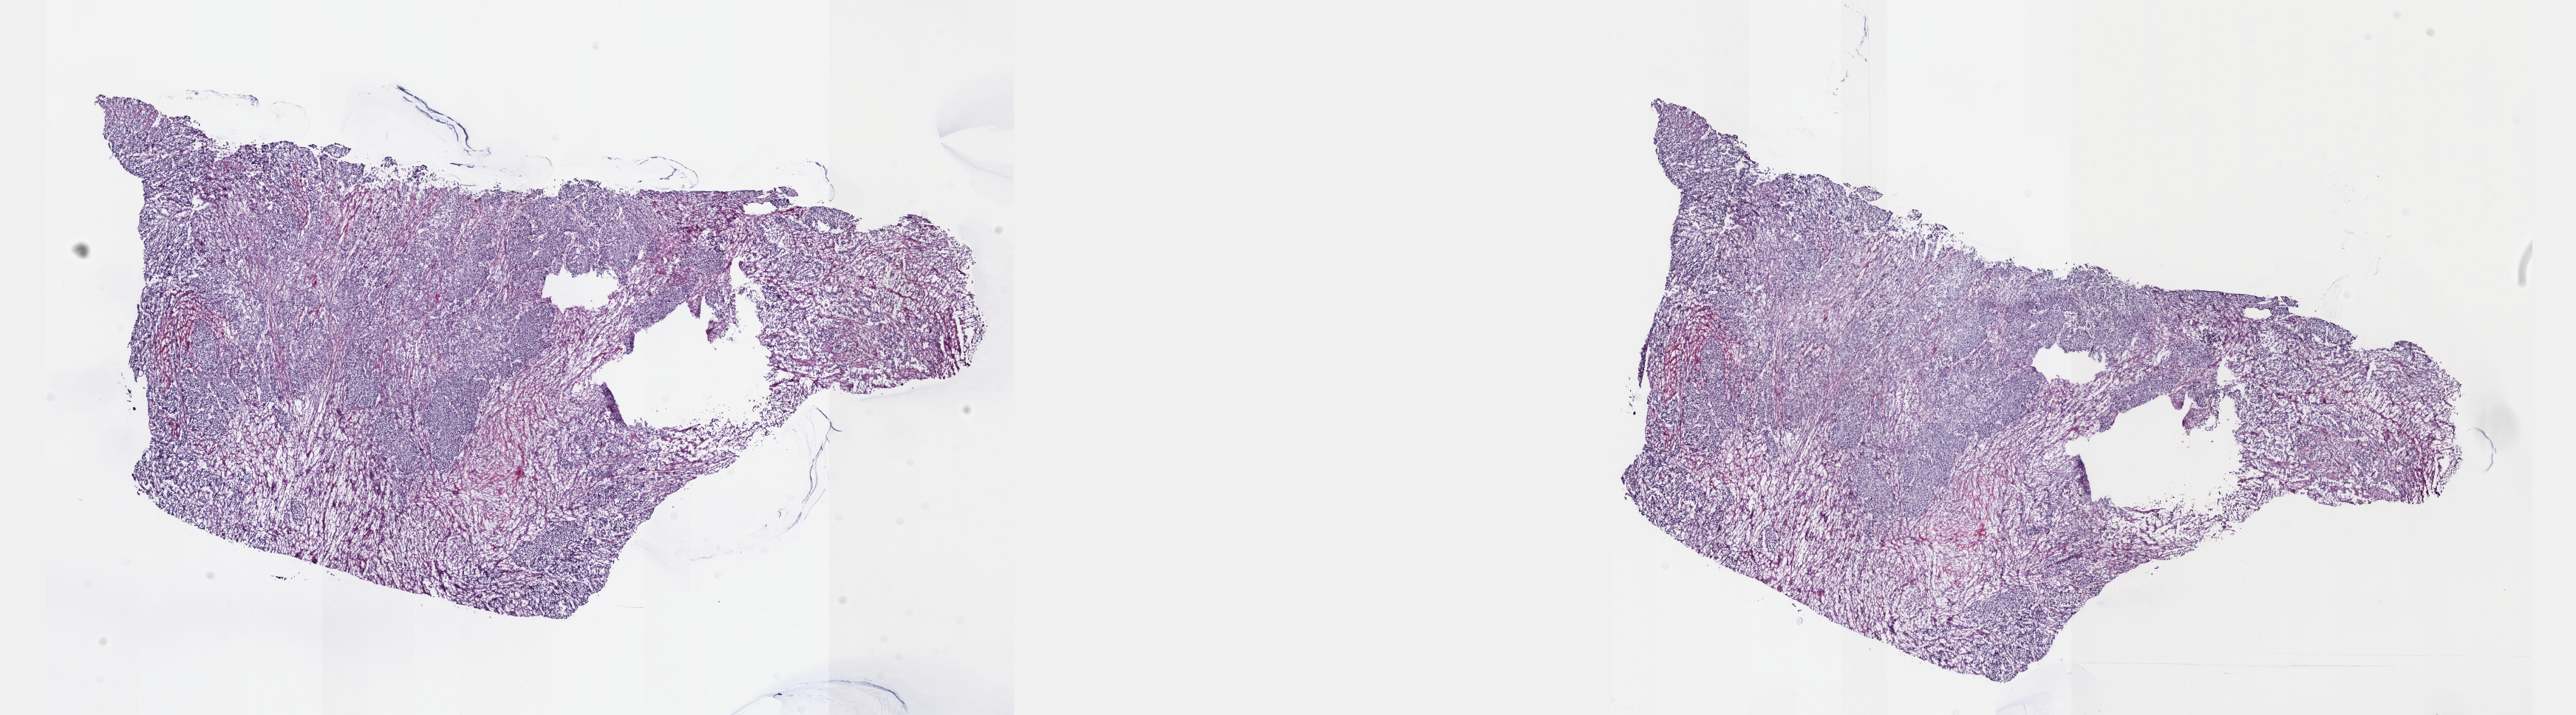
H&E whole-slide image — low-resolution overview of the scanned area, about 28.2 x 7.8 mm, frozen section from the top of the tissue portion, primary tumour sample from the bladder. Male, age 79 years at initial diagnosis. Histologic grade: high grade. Pathologist review of this section (percent, as recorded): tumour cells 70%, tumour nuclei 80%, normal cells 10%, stromal cells 20%, necrosis 0%. Inflammatory infiltration, as recorded: lymphocyte infiltration 0%, monocyte infiltration 0%, neutrophil infiltration 0%.
- AJCC pathologic stage: IV (5th edition)
- histologic diagnosis: Transitional cell carcinoma
- lymph nodes positive (case pathology): 6 of 107 examined